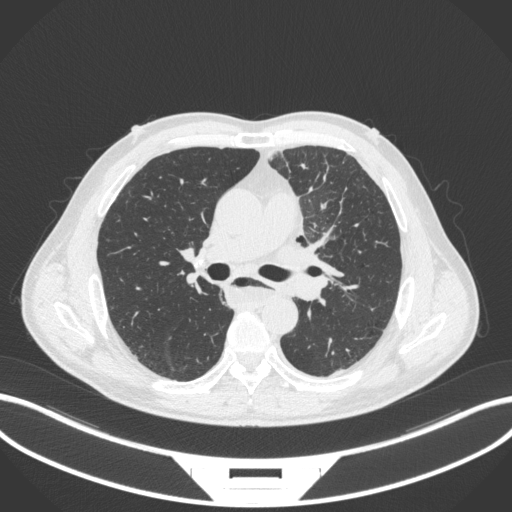
Chest CT, one axial slice. Slice 227 of 411 in the series (ordered by position). 120 kVp. Lung window (W 1500 / L -600 HU). 1 mm slice thickness. 512 × 512 image matrix. Patient: male, 57 years. From the clinical record (not read from this slice): clinical TNM (as recorded): T2a N1 M0.
Outlined on this slice (rectangle marked by the reading radiologist):
- lung tumour (recorded histology: squamous cell carcinoma): bounding box [x1, y1, x2, y2] px = [276, 239, 336, 282]